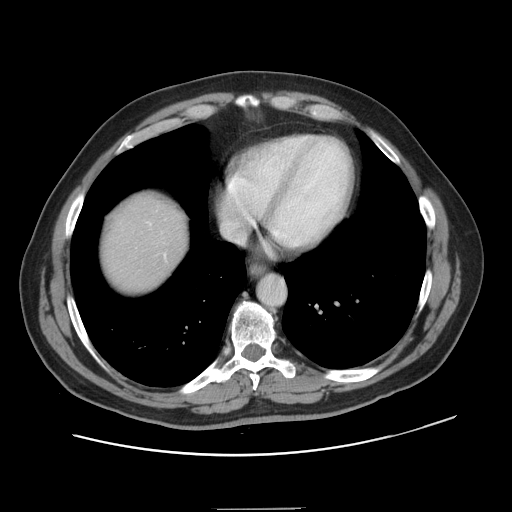
Contrast-enhanced abdominal CT, one axial slice; position 137 of 143 along the scan axis; 120 kVp; intravenous contrast given; soft-tissue window (W 400 / L 40 HU); 2.5 mm slice thickness; 512 × 512 image matrix. Male patient, age 62 years. From the clinical record (not read from this slice): diagnosis: colorectal cancer liver metastases, imaged before liver resection; multiple liver metastases: yes; largest metastasis: 2.7 cm; disease in both lobes: no.
Annotated regions visible in this slice (outlined manually by an expert reader):
- liver: bounding box (x1, y1, x2, y2) in pixels: (104, 197, 186, 291)
- planned liver remnant (the part of the liver to remain after resection): (104, 197, 186, 291)